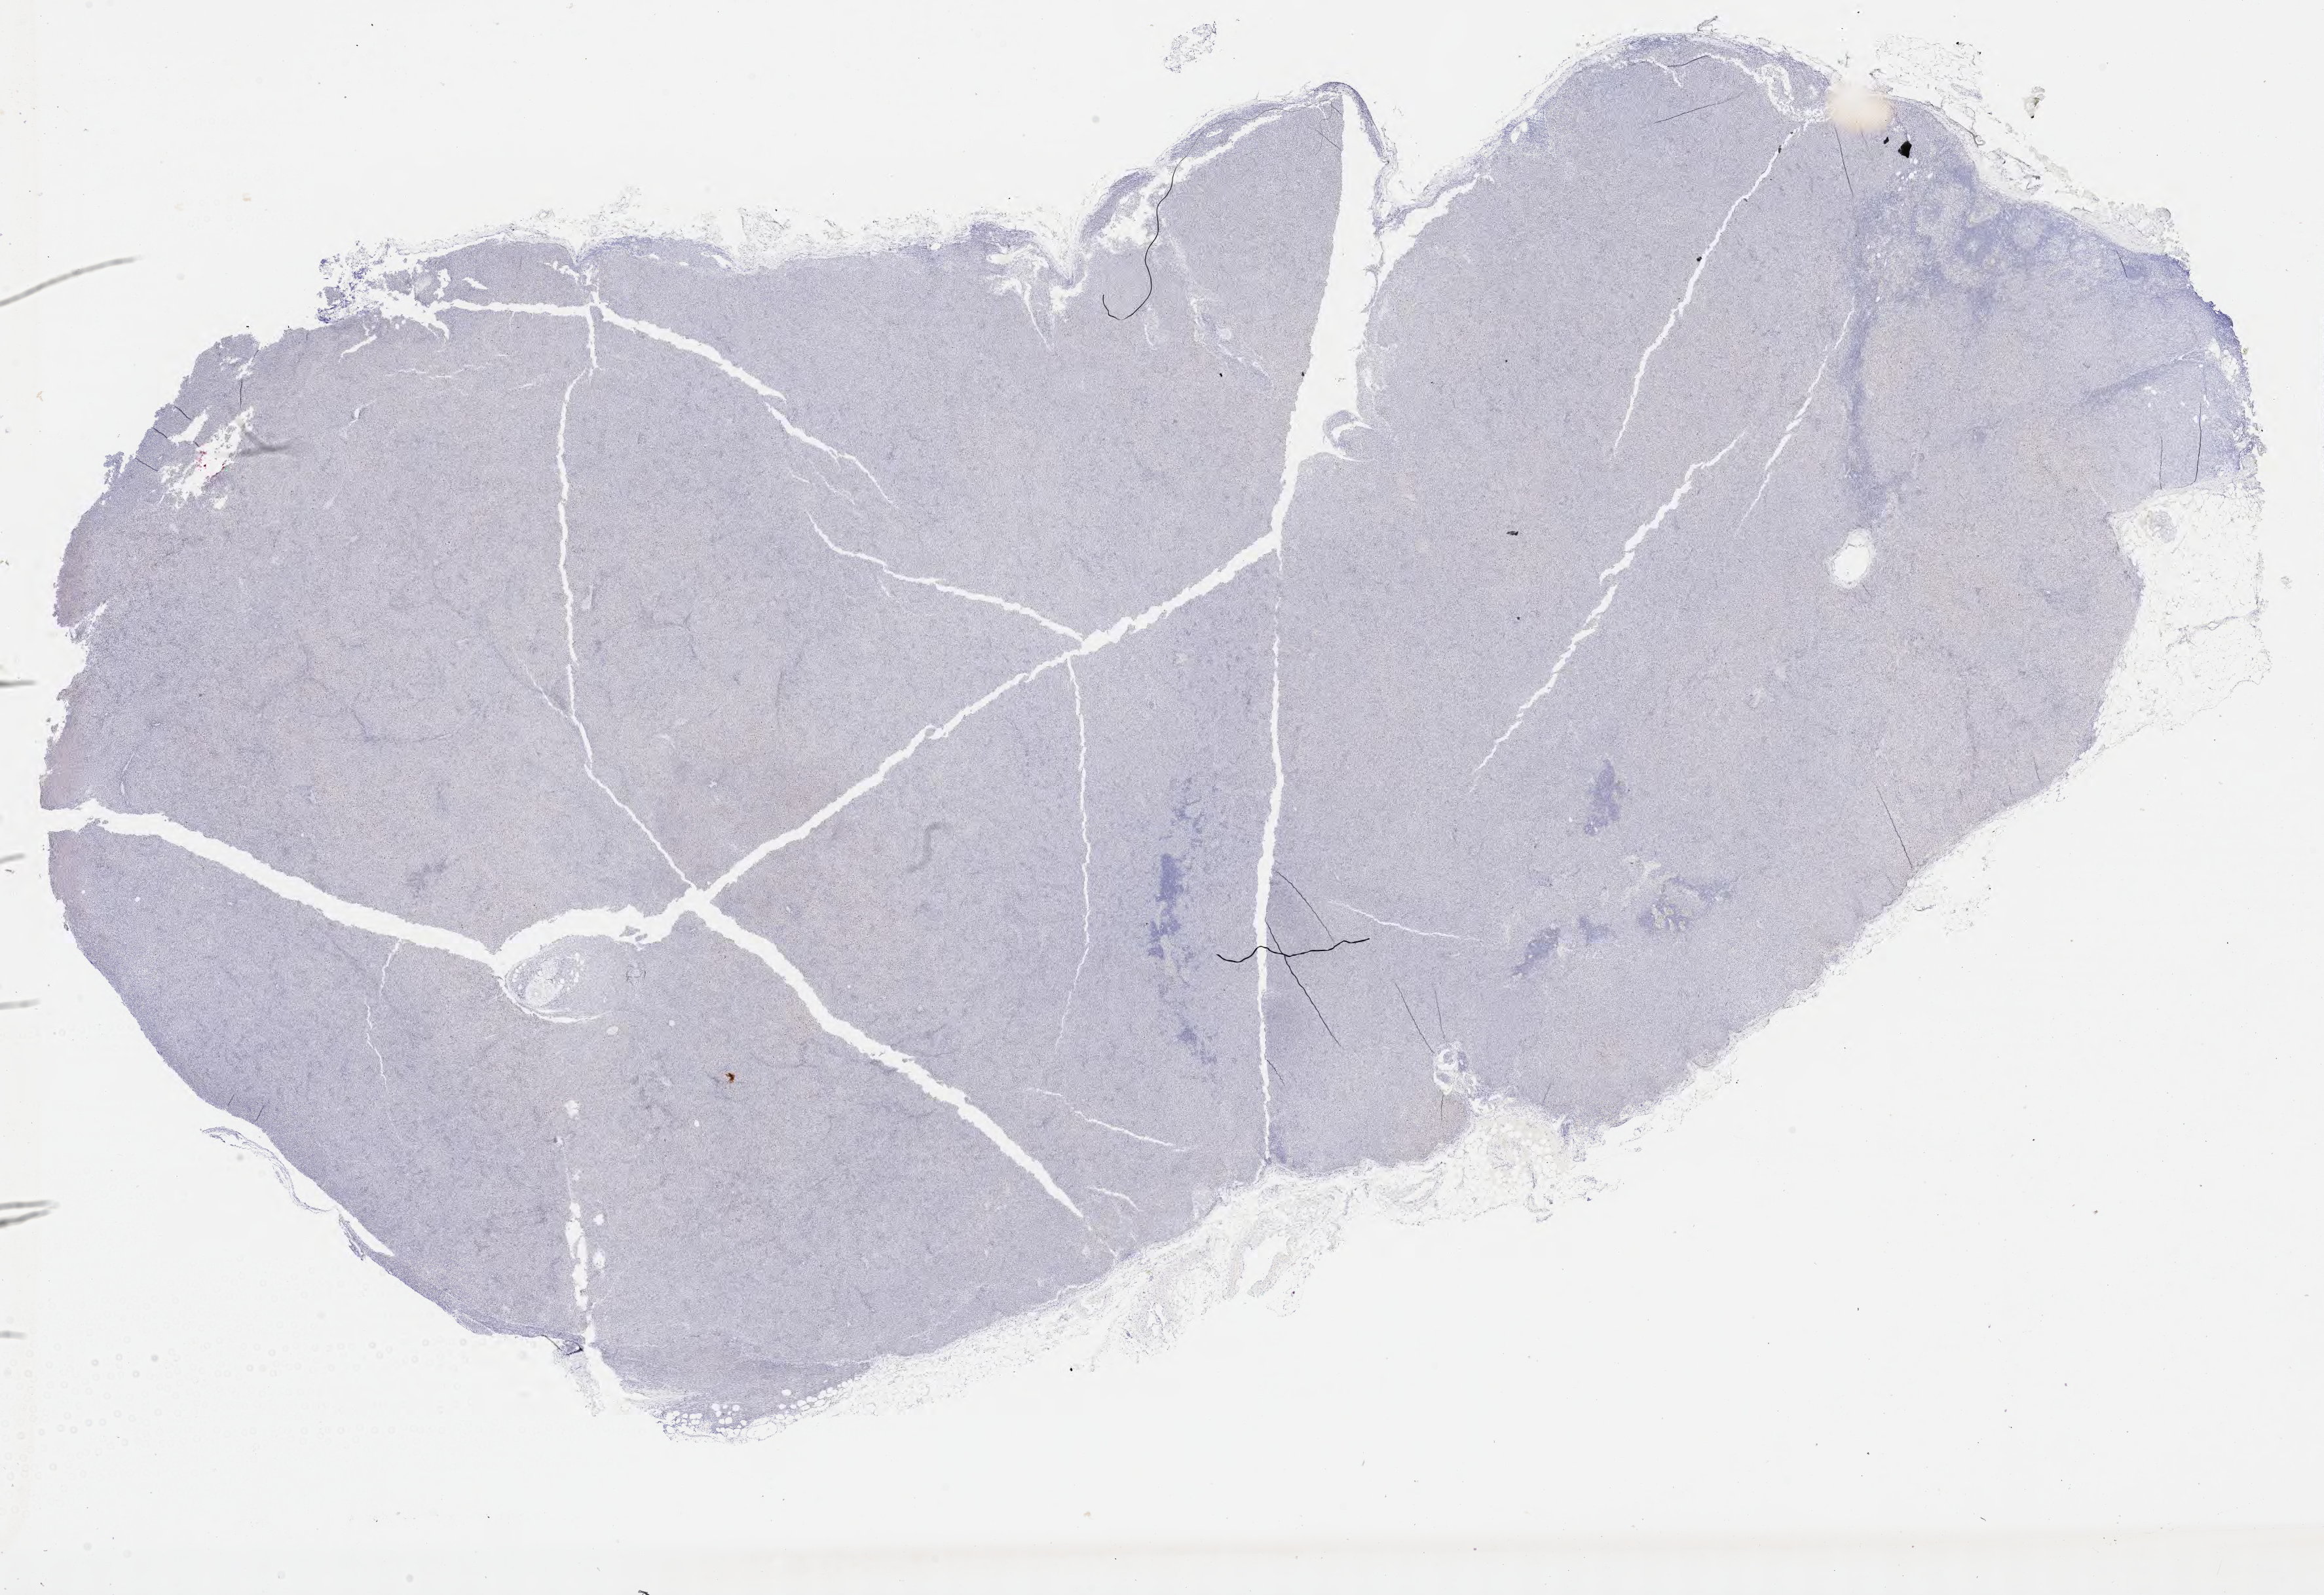
Immunohistochemistry (IHC) whole-slide image stained for p53, whole scanned area (about 28.7 x 19.7 mm) shown as a low-resolution overview, tumor tissue. Patient: male, age 69 years.
Diagnosis: Diffuse large B-cell lymphoma, NOS.